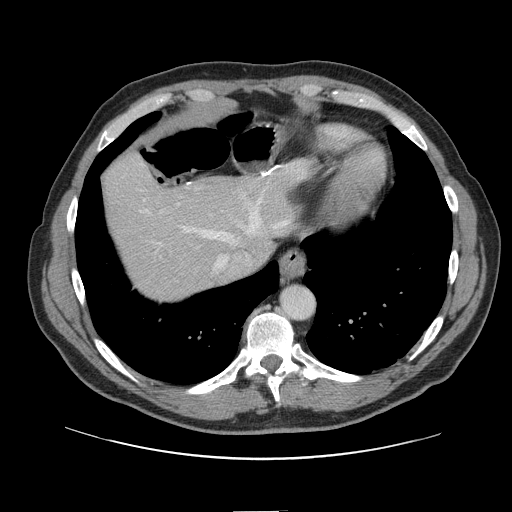
Contrast-enhanced abdominal CT, one axial slice; position 124 of 161 along the scan axis; 120 kVp; soft-tissue window (W 400 / L 40 HU); 2.5 mm slice thickness; 512 × 512 image matrix, field of view 412 × 412 mm. Male patient, age 66 years. Case-level facts recorded for this patient, not image findings: diagnosis: colorectal cancer liver metastases, imaged before liver resection; multiple liver metastases: no; largest metastasis: 3.5 cm; chemotherapy before resection: yes.
Outlined on this slice (outlined manually by an expert reader):
- hepatic veins: bounding box <141,195,290,273> (left, top, right, bottom; pixels)
- liver: <104,155,306,300>
- planned liver remnant (the part of the liver to remain after resection): <104,156,308,293>